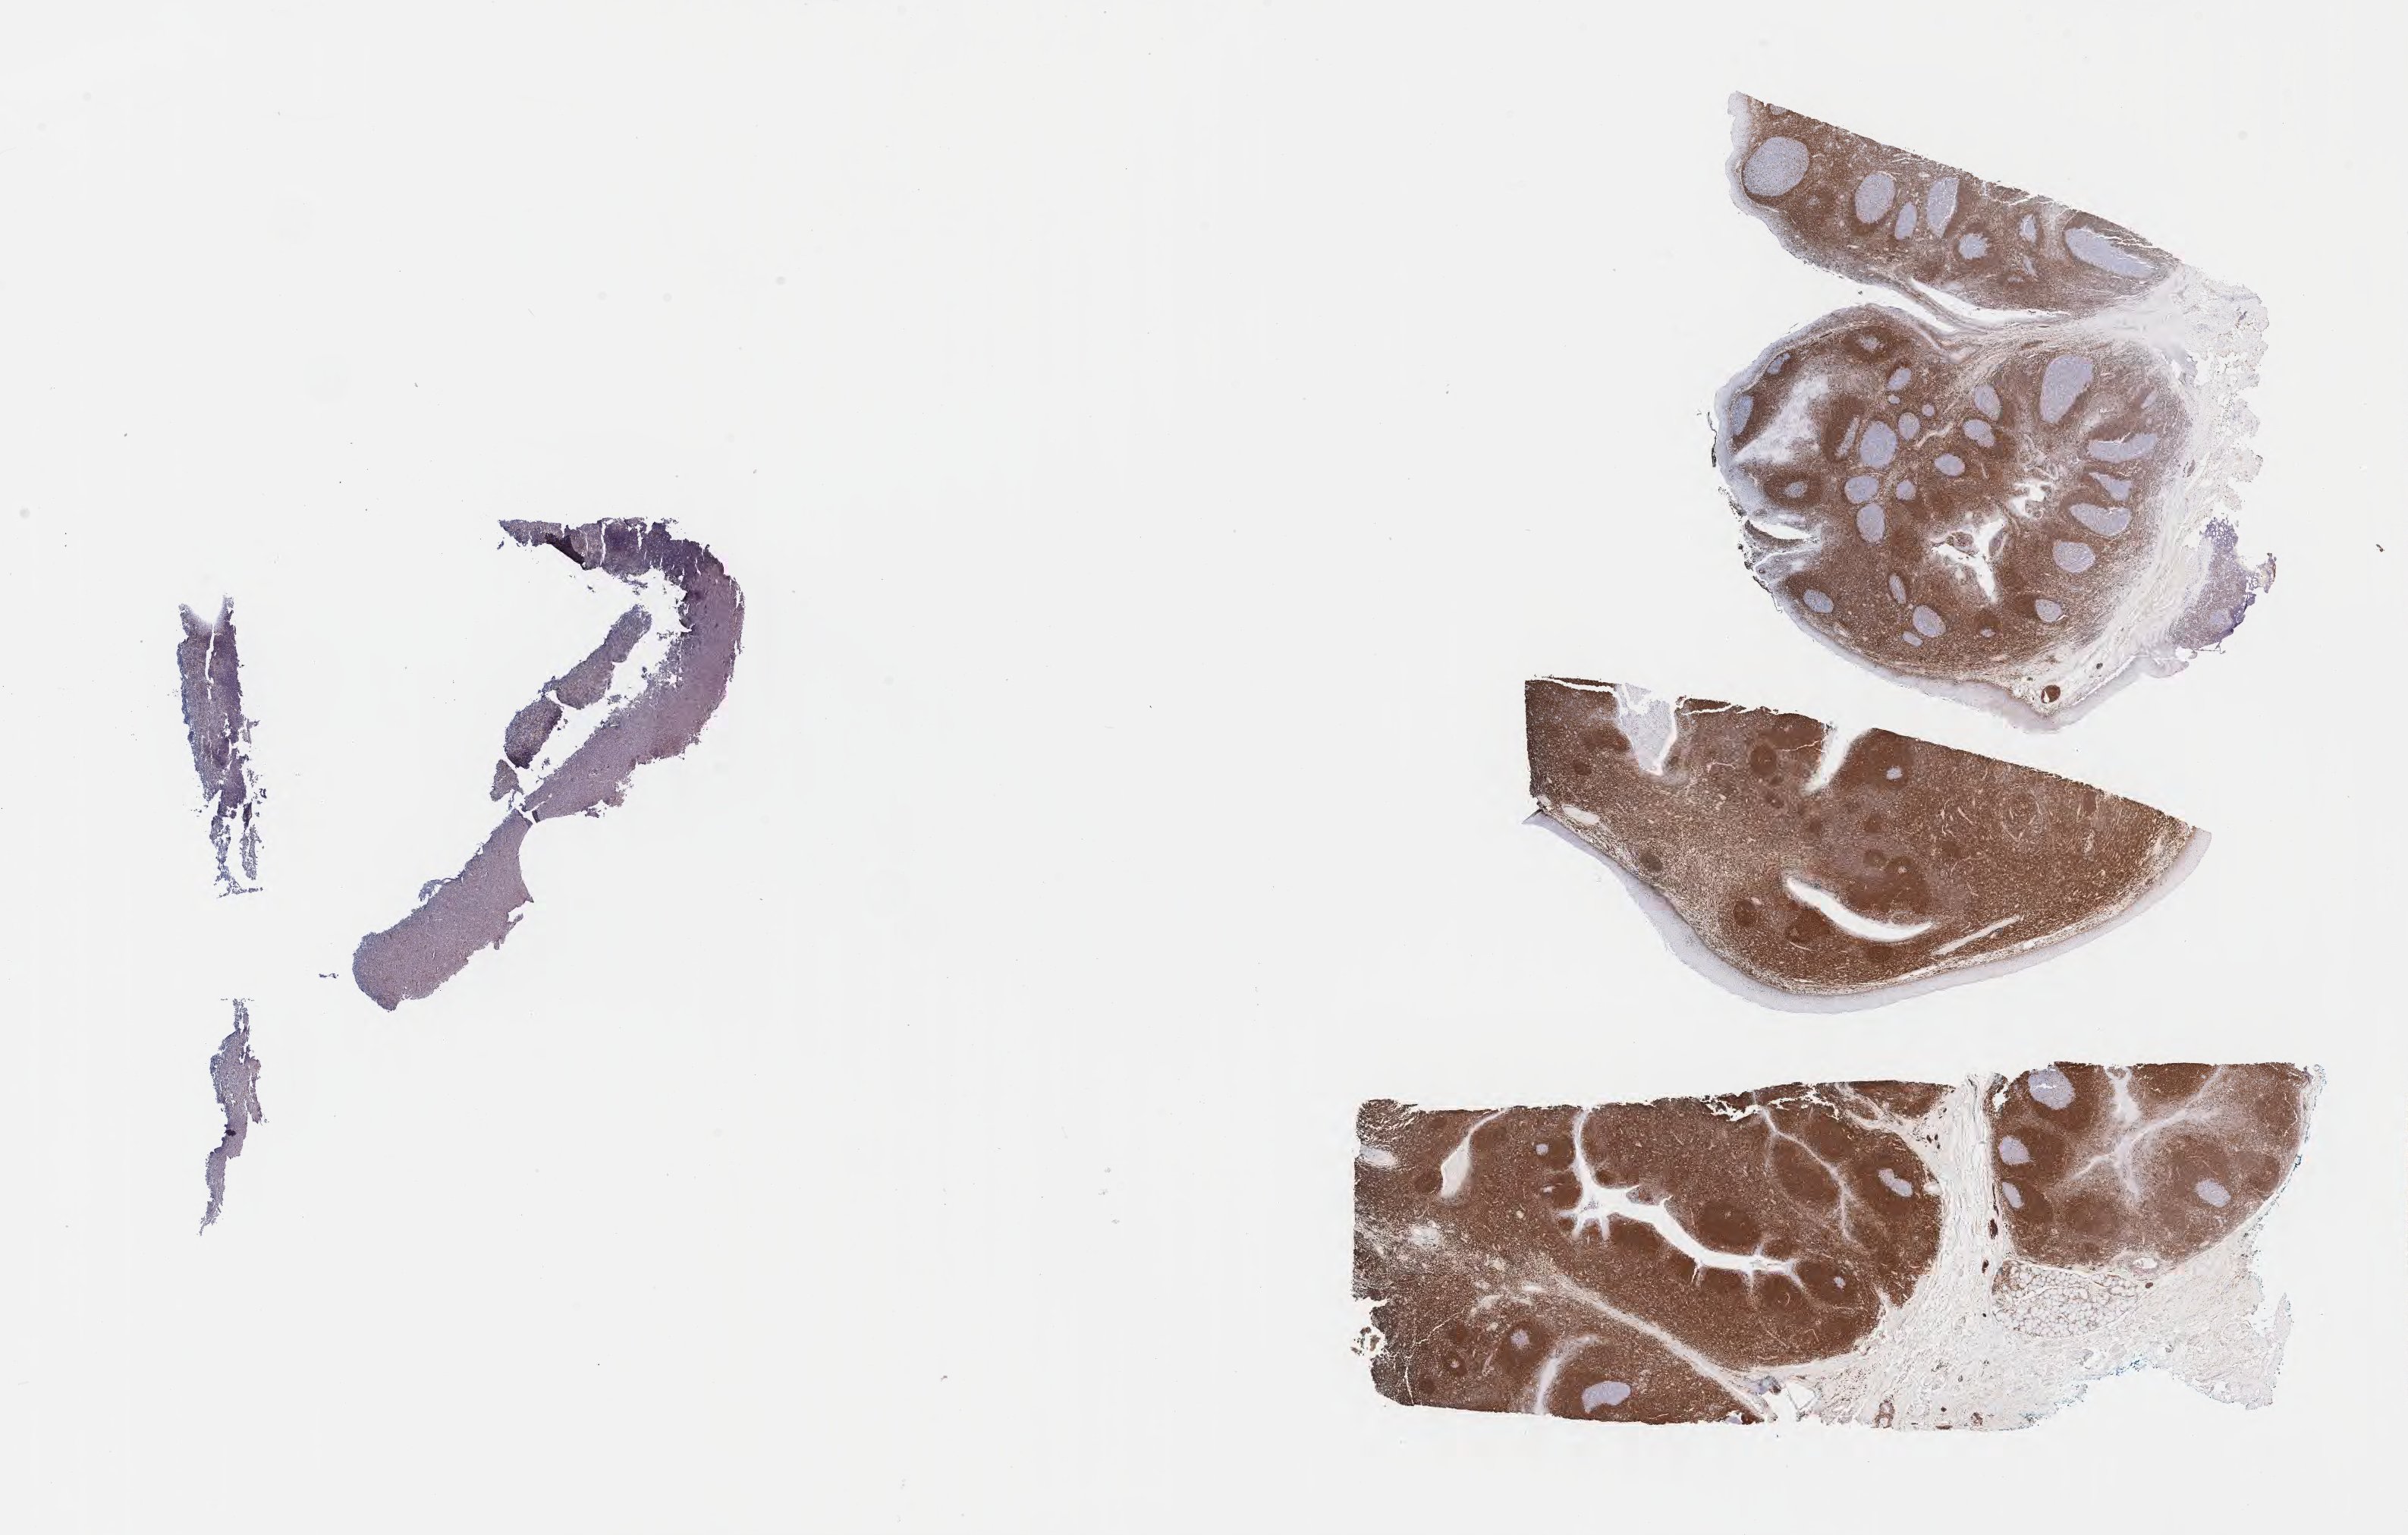
Immunohistochemistry (IHC) whole-slide image stained for BCL2, whole scanned area (about 25.7 x 16.3 mm) shown as a low-resolution overview, tumor tissue, site: peritoneum. Female, age 7 years at initial diagnosis.
Diagnosis: Burkitt lymphoma, NOS.